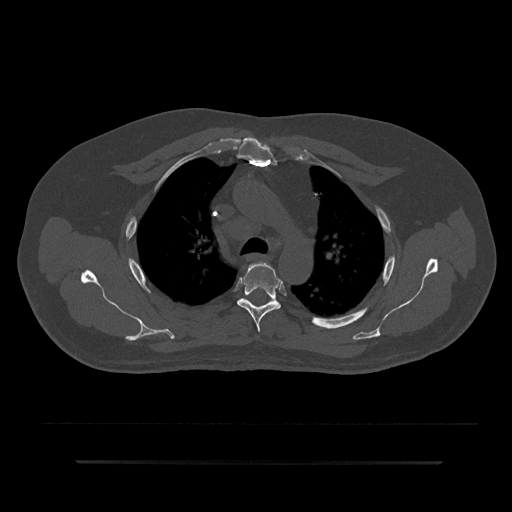
CT including the spine, one axial slice; position 615 of 797 along the scan axis; reconstruction kernel Br40s/3; bone window (W 1800 / L 400 HU); 0.5 mm slice thickness; 512 × 512 image matrix, field of view 464 × 464 mm. Patient: male, 59 years. Case-level facts recorded for this patient, not image findings: primary cancer: bile ducts; vertebrae with lytic lesions (as recorded): T10.
Structures marked on this image (semi-automatically segmented with operator editing):
- T4 vertebra: bounding box (x1, y1, x2, y2) in pixels: (237, 262, 283, 332)
- T5 vertebra: (238, 298, 277, 303)